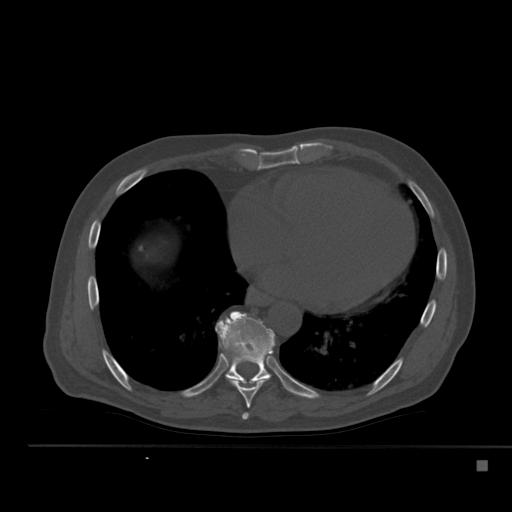
CT including the spine, one axial slice. Slice 299 of 517 in the series (ordered by position). Reconstruction kernel Br40s. Bone window (W 1800 / L 400 HU). 1.5 mm slice thickness. 512 × 512 image matrix, field of view 408 × 408 mm. Male patient, age 70 years. Case-level facts recorded for this patient, not image findings: primary cancer: renal; vertebrae with lytic lesions (as recorded): T4, T6, T10, T12, L3, L4, L5.
Structures marked on this image (semi-automatic segmentation, software-assisted and operator-edited):
- T7 vertebra: box from (x=242, y=413) to (x=249, y=420) px
- T8 vertebra: (x=219, y=343)–(x=270, y=408)
- T9 vertebra: (x=215, y=311)–(x=276, y=383)